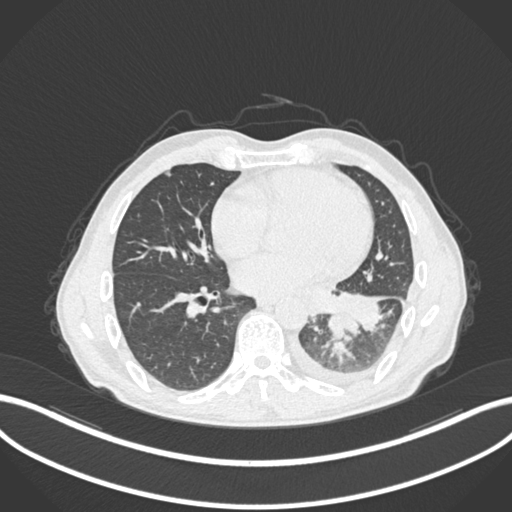
Chest CT, one axial slice; position 100 of 222 along the scan axis; reconstruction kernel B30f; lung window (W 1500 / L -600 HU); 1 mm slice thickness; 512 × 512 image matrix, field of view 400 × 400 mm. Patient: male, 47 years. From the clinical record (not read from this slice): clinical TNM (as recorded): T3 N1 M1c; histopathological grade: G3.
Annotated regions visible in this slice (rectangle marked by the reading radiologist):
- lung tumour (recorded histology: small cell carcinoma): bounding box [x1, y1, x2, y2] px = [325, 308, 361, 342]